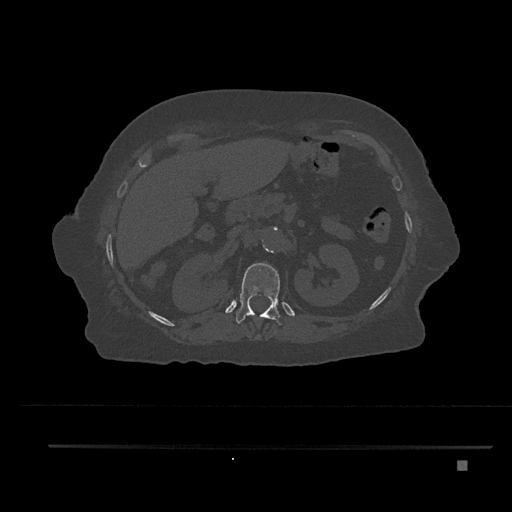
CT including the spine, one axial slice. Slice 266 of 797 in the series (ordered by position). Reconstruction kernel Br40s/3. 120 kVp. Bone window (W 1800 / L 400 HU). 512 × 512 image matrix, field of view 437 × 437 mm. Female patient, age 76 years. From the clinical record (not read from this slice): primary cancer: lung; vertebrae with lytic lesions (as recorded): T11, L3.
Annotated regions visible in this slice (semi-automatically segmented with operator editing):
- T12 vertebra: box from (x=236, y=263) to (x=282, y=337) px